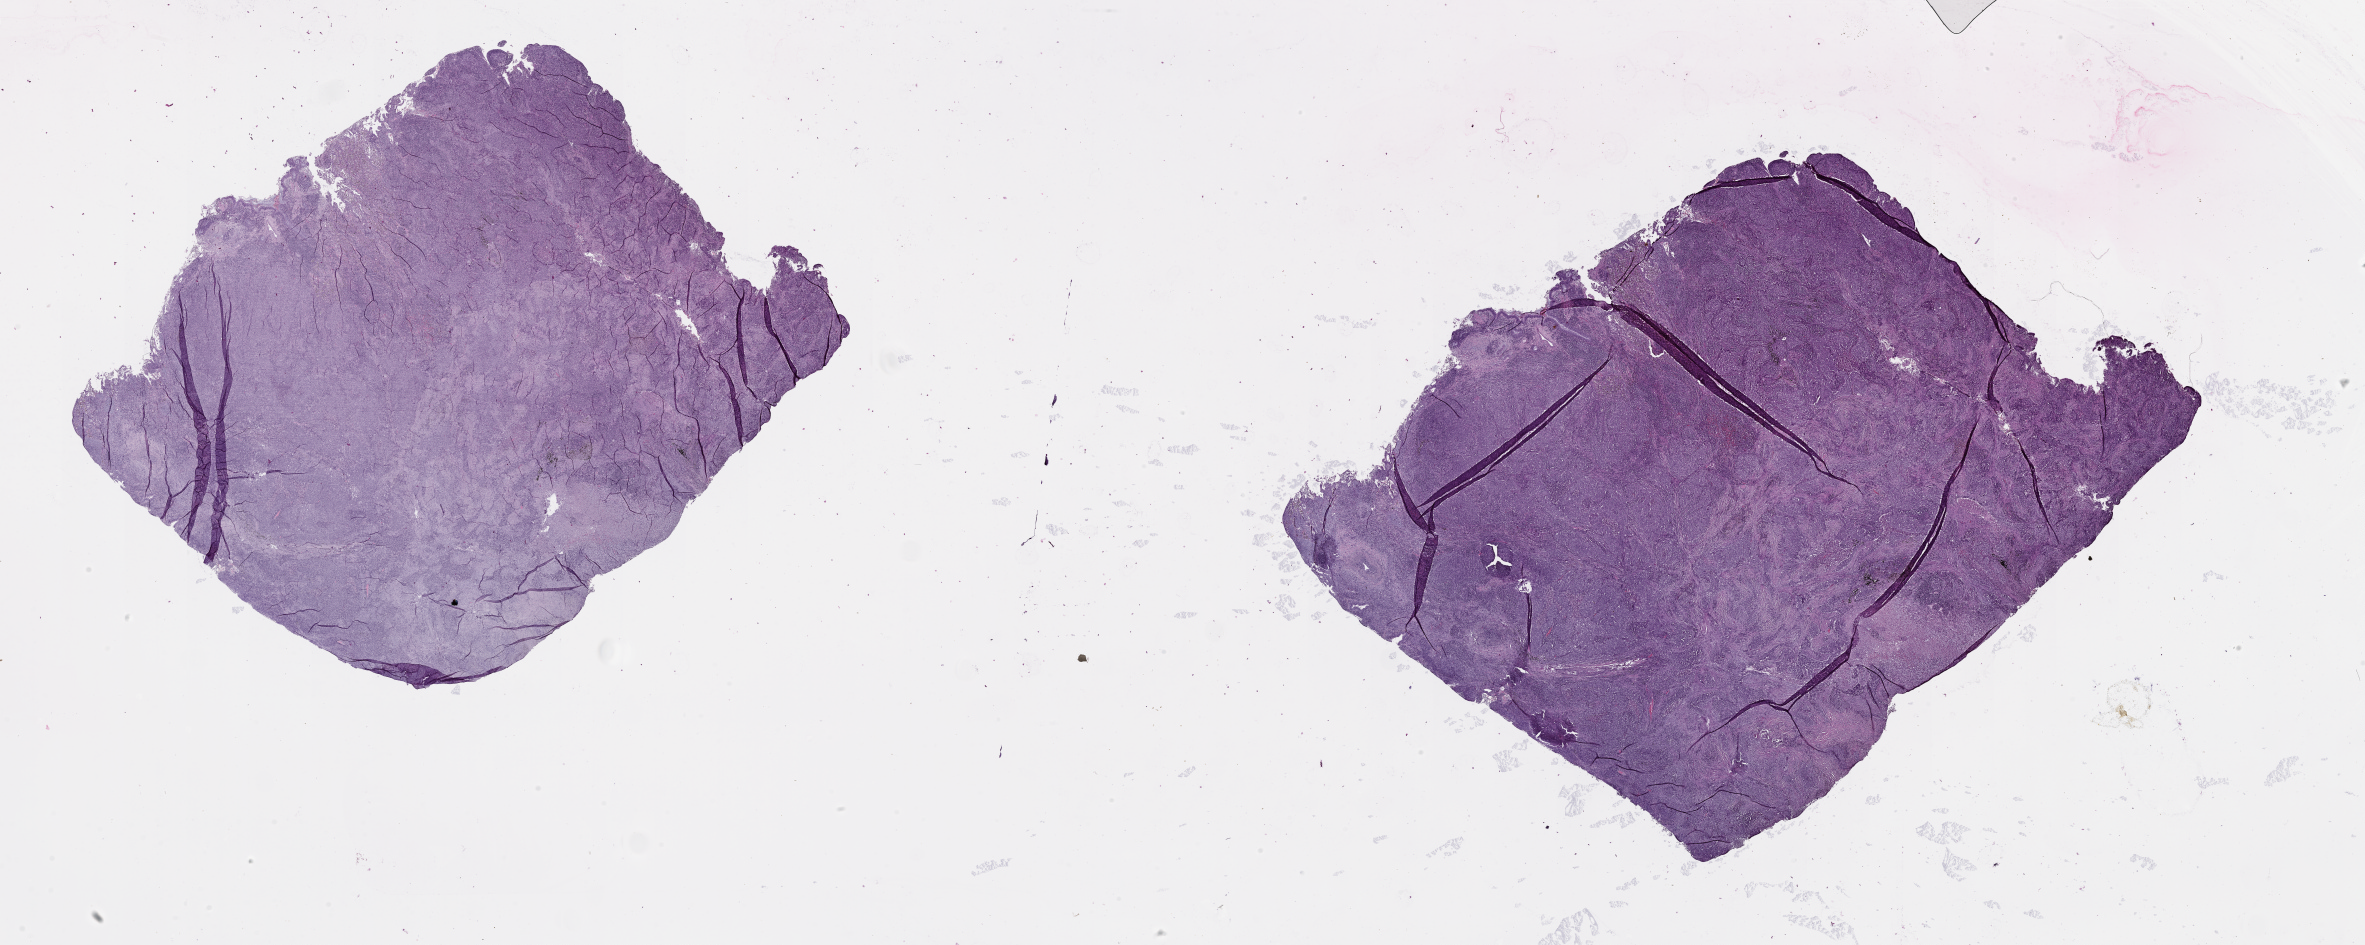
Whole-slide histology image, H&E-stained — low-resolution overview of the scanned area, about 38.1 x 15.2 mm (from a 20x scan). Tumour tissue sample, lung. Male, 65 y/o.
Patient diagnosis (cohort enrolment): squamous cell carcinoma (lung).